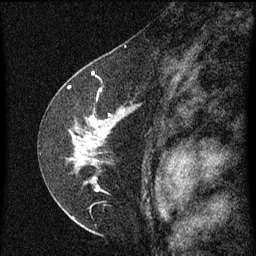
Breast MRI (dynamic contrast-enhanced), one sagittal slice; dynamic contrast-enhanced series, image 2 of 3 at this slice position (ordered by acquisition); 1.5 T; TE 4.2 ms, TR 8 ms; 256 × 256 image matrix, field of view 180 × 180 mm. Female patient, age 47 years.
Outlined on this slice (semi-automatic segmentation, software-assisted and operator-edited):
- analysis volume of interest (the breast-tissue region the enhancement analysis was run in; not a lesion): bounding box <48,84,139,199> (left, top, right, bottom; pixels)
- tumour enhancement mask (voxels above the 70 % enhancement threshold inside the analysis volume of interest): <90,110,125,191>